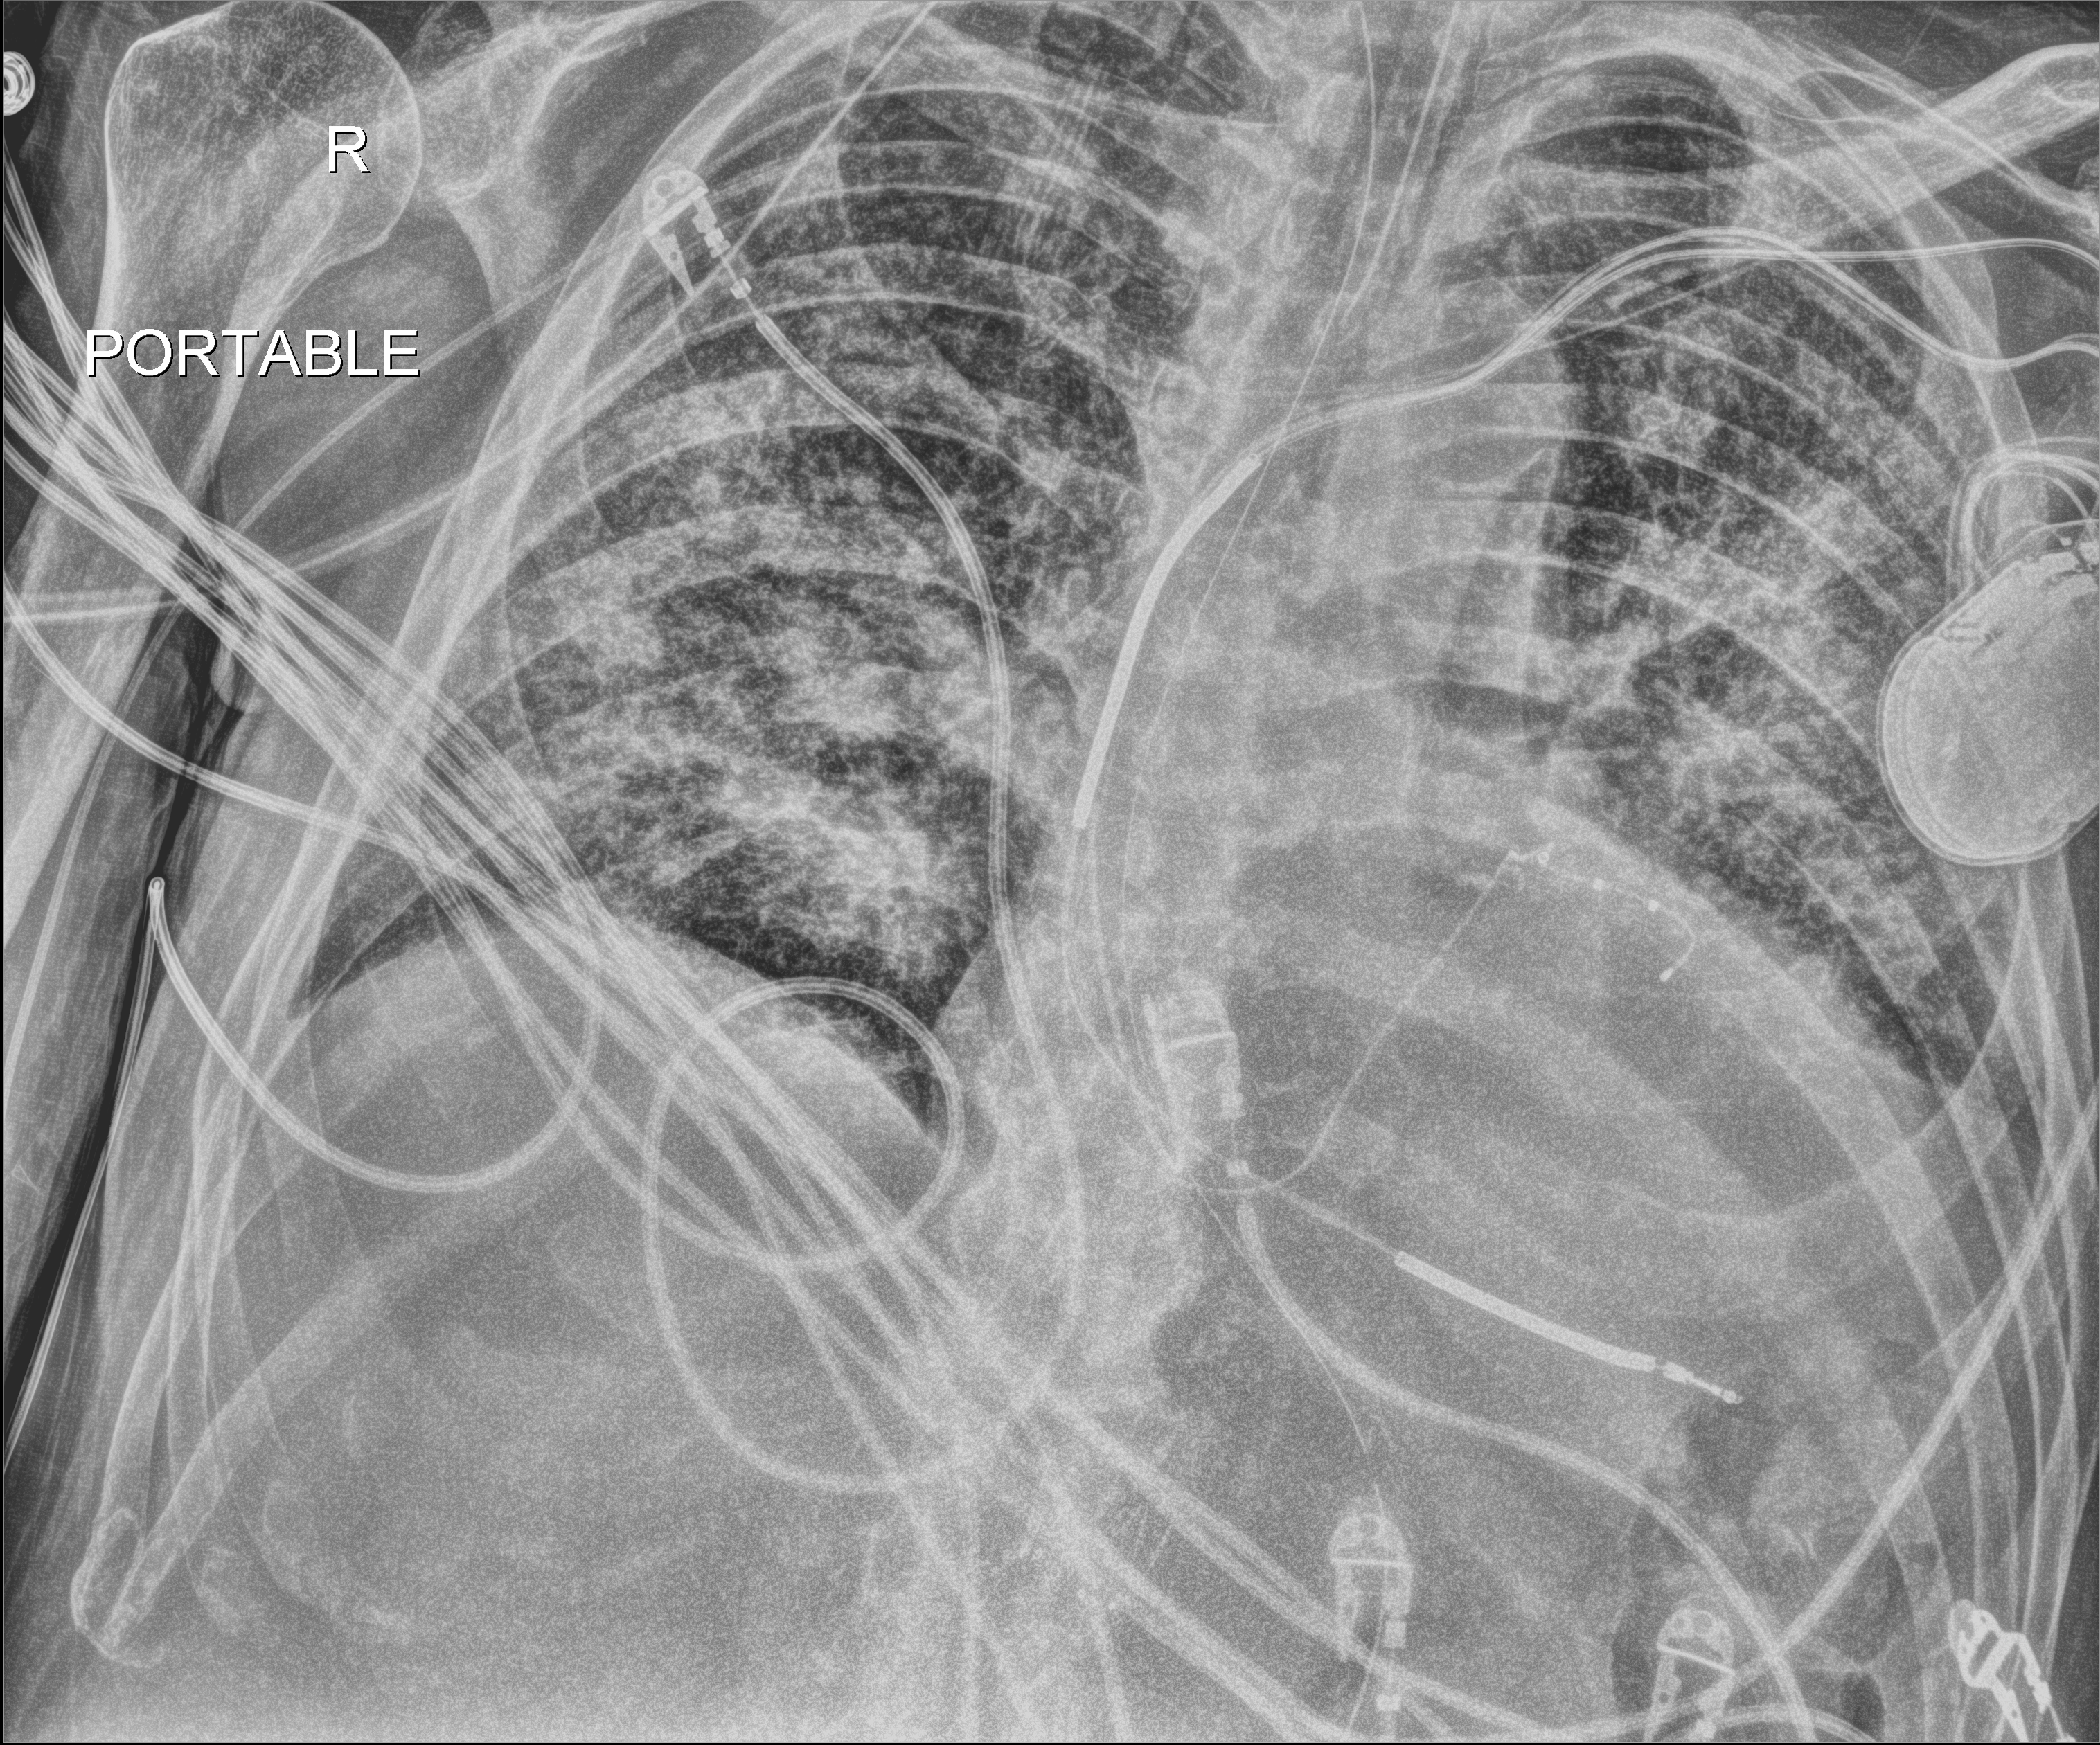
Chest X-ray (portable), anteroposterior (AP) projection. Male patient hospitalised with COVID-19, age 60–74 years.
From the hospital-stay record, not from the radiograph (when in the stay this image was taken is not recorded):
- admitted to intensive care during this hospital stay: yes
- mechanically ventilated during this hospital stay: yes
- length of hospital stay: 36 days